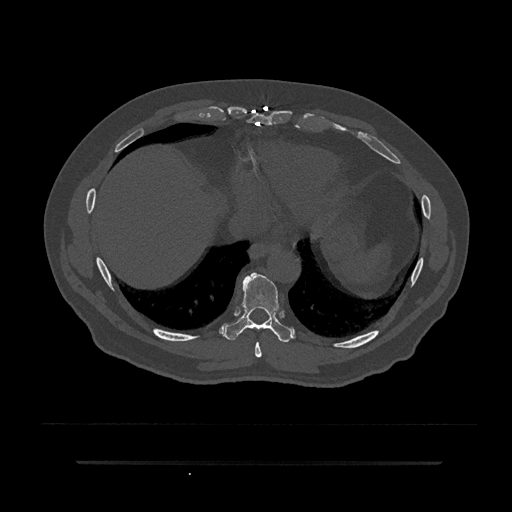
CT including the spine, one axial slice. Slice 386 of 797 in the series (ordered by position). Reconstruction kernel Br40s/3. 120 kVp. Bone window (W 1800 / L 400 HU). 0.5 mm slice thickness. 512 × 512 image matrix. Male patient, age 59 years. Case-level facts recorded for this patient, not image findings: primary cancer: bile ducts; vertebrae with lytic lesions (as recorded): T10.
Annotated regions visible in this slice (semi-automatic segmentation, software-assisted and operator-edited):
- T8 vertebra: bounding box <255,342,262,358> (left, top, right, bottom; pixels)
- T9 vertebra: <224,272,292,343>